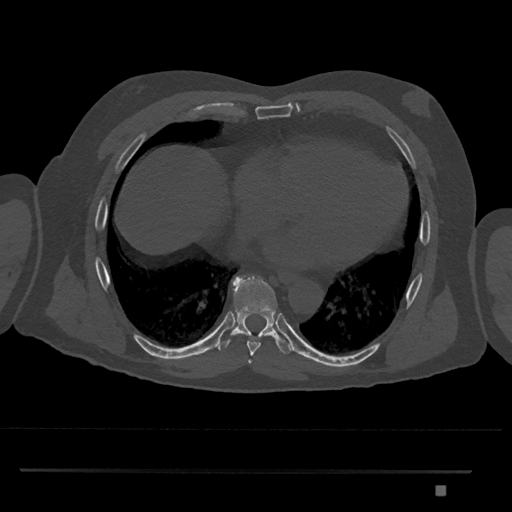
CT including the spine, one axial slice; position 1132 of 1134 along the scan axis; 120 kVp; bone window (W 1800 / L 400 HU); 0.5 mm slice thickness; 512 × 512 image matrix, field of view 429 × 429 mm. Patient: male, 65 years. From the clinical record (not read from this slice): primary cancer: prostate.
Structures marked on this image (semi-automatically segmented with operator editing):
- T8 vertebra: box from (x=216, y=276) to (x=292, y=356) px